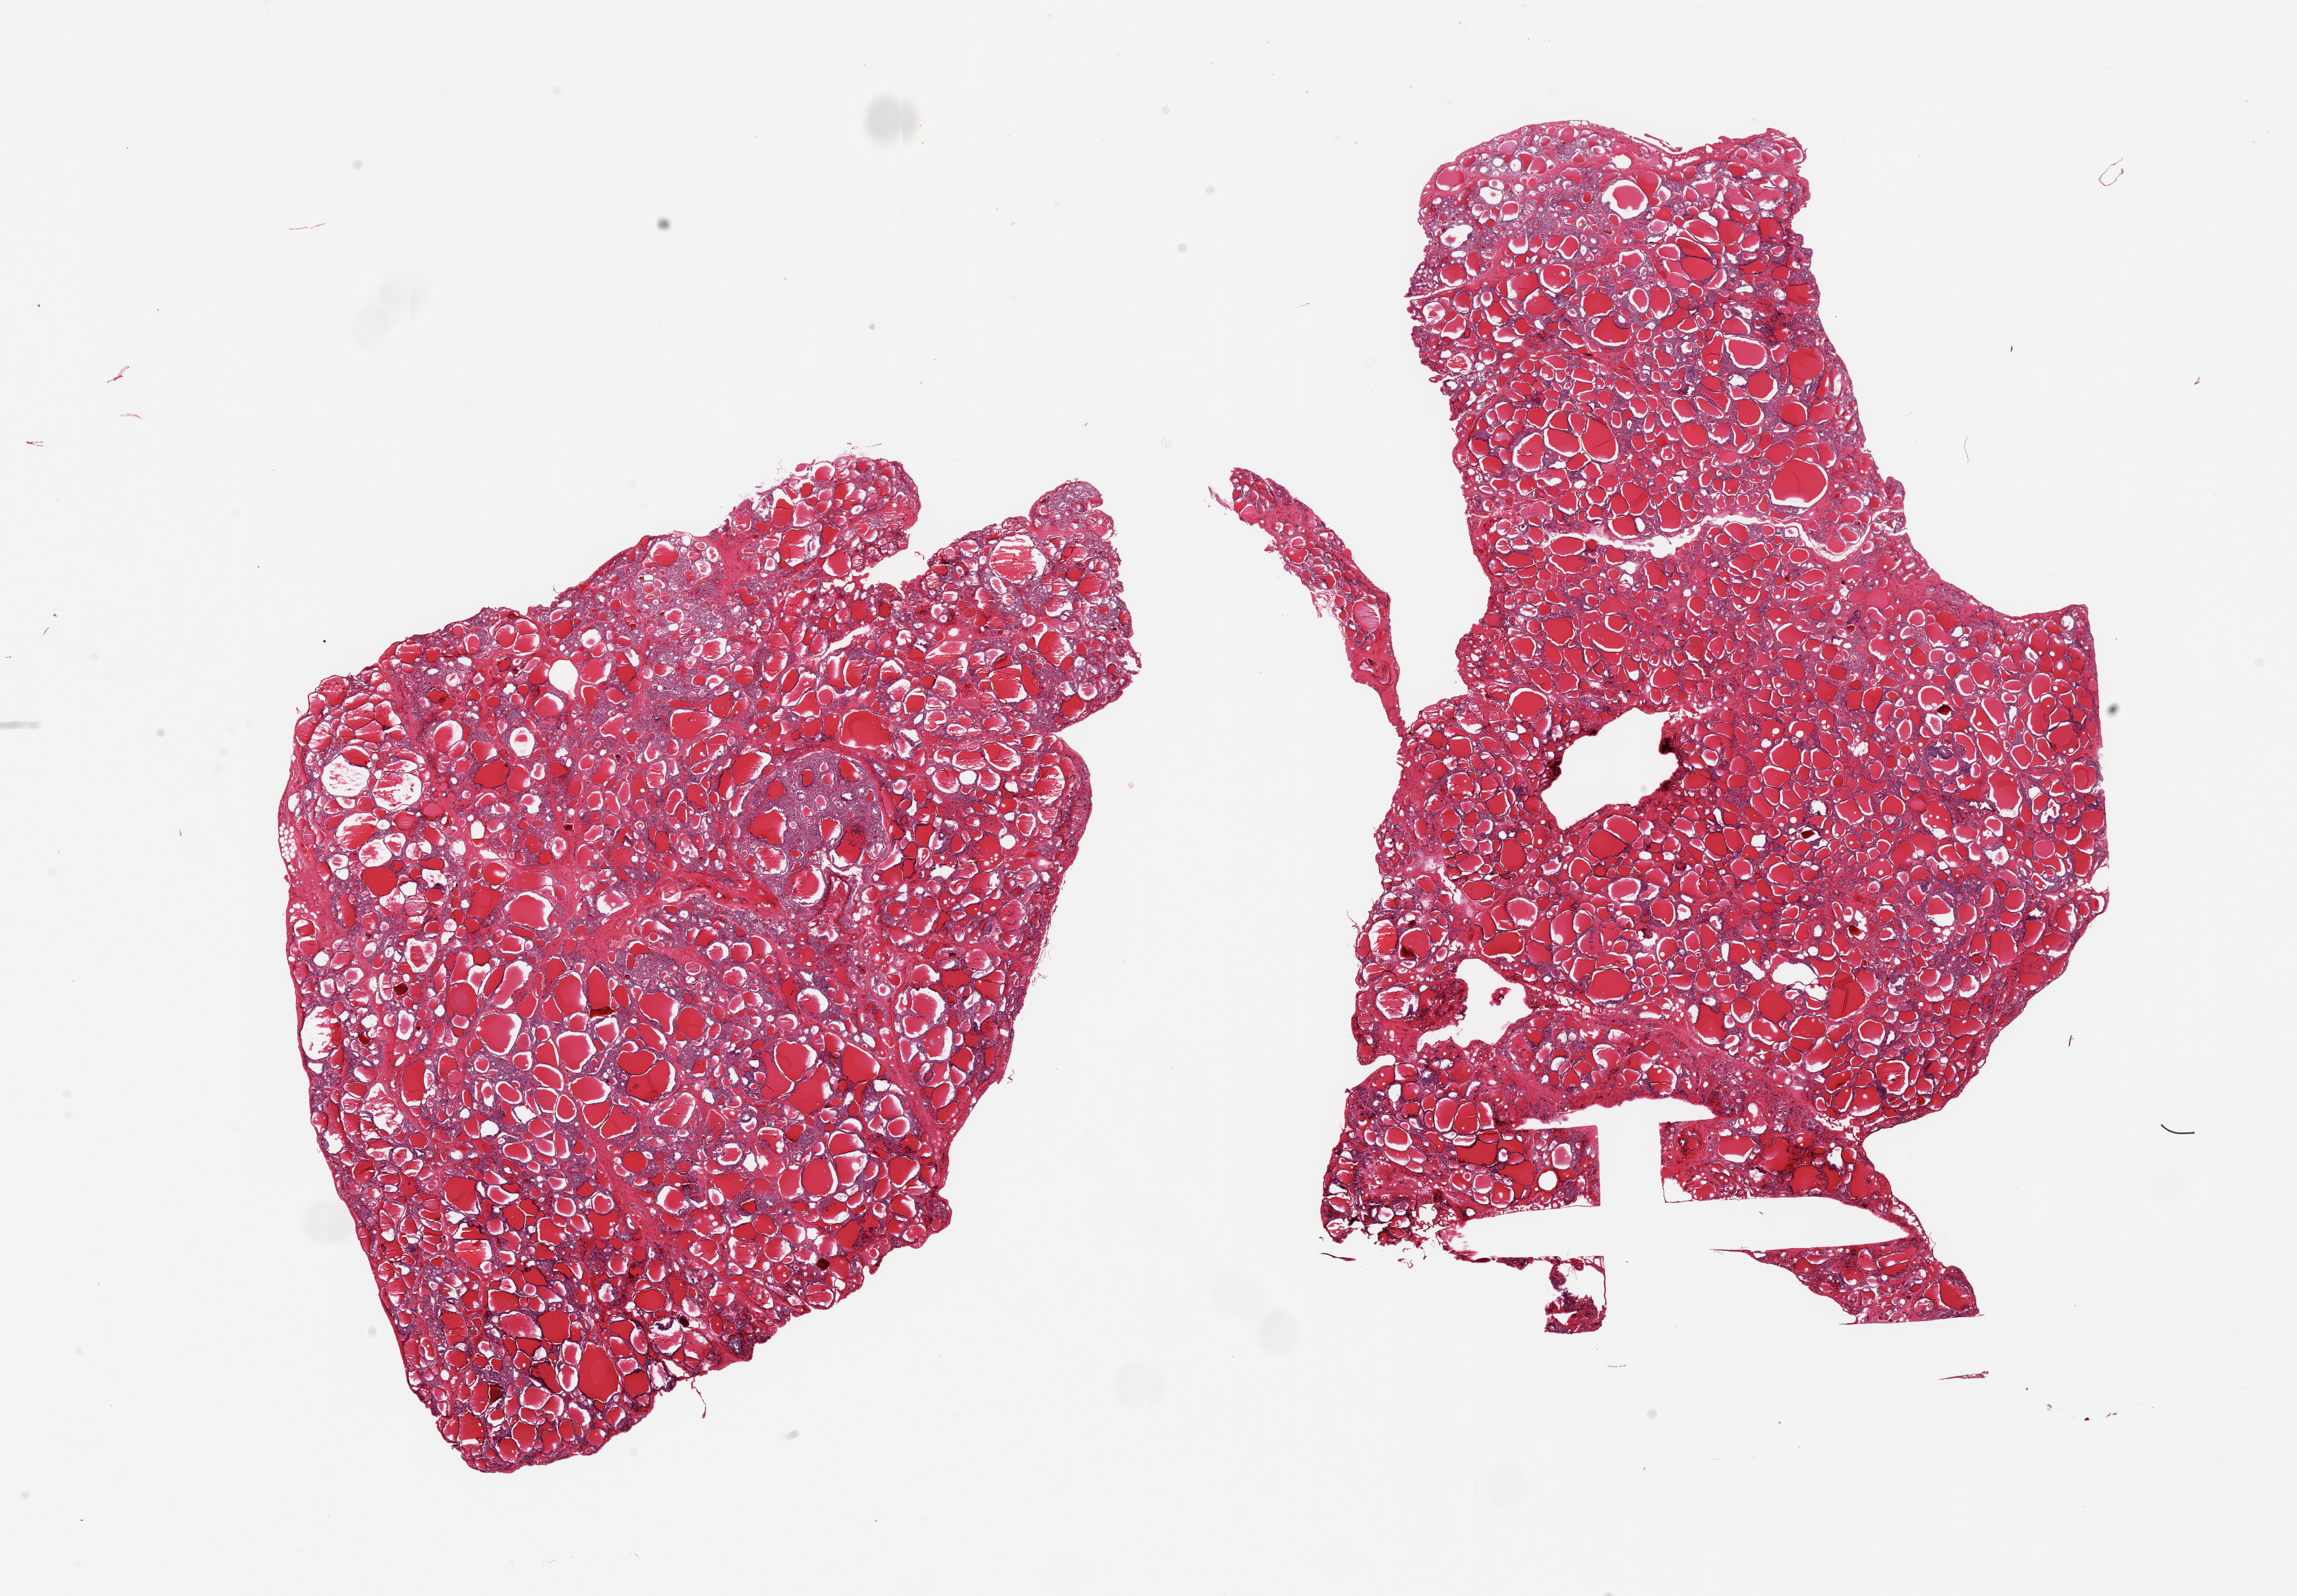
Hematoxylin and eosin (H&E) whole-slide image — whole scanned area (about 27.6 x 19.2 mm, slide scanned at 20x) shown as a low-resolution overview. PAXgene-fixed, paraffin-embedded tissue. Target tissue: thyroid. Donor tissue sample. Donor: male.
Pathologist's review note for this sample: 2 pieces, microfollicular adenomatoid nodule, ~2mm.